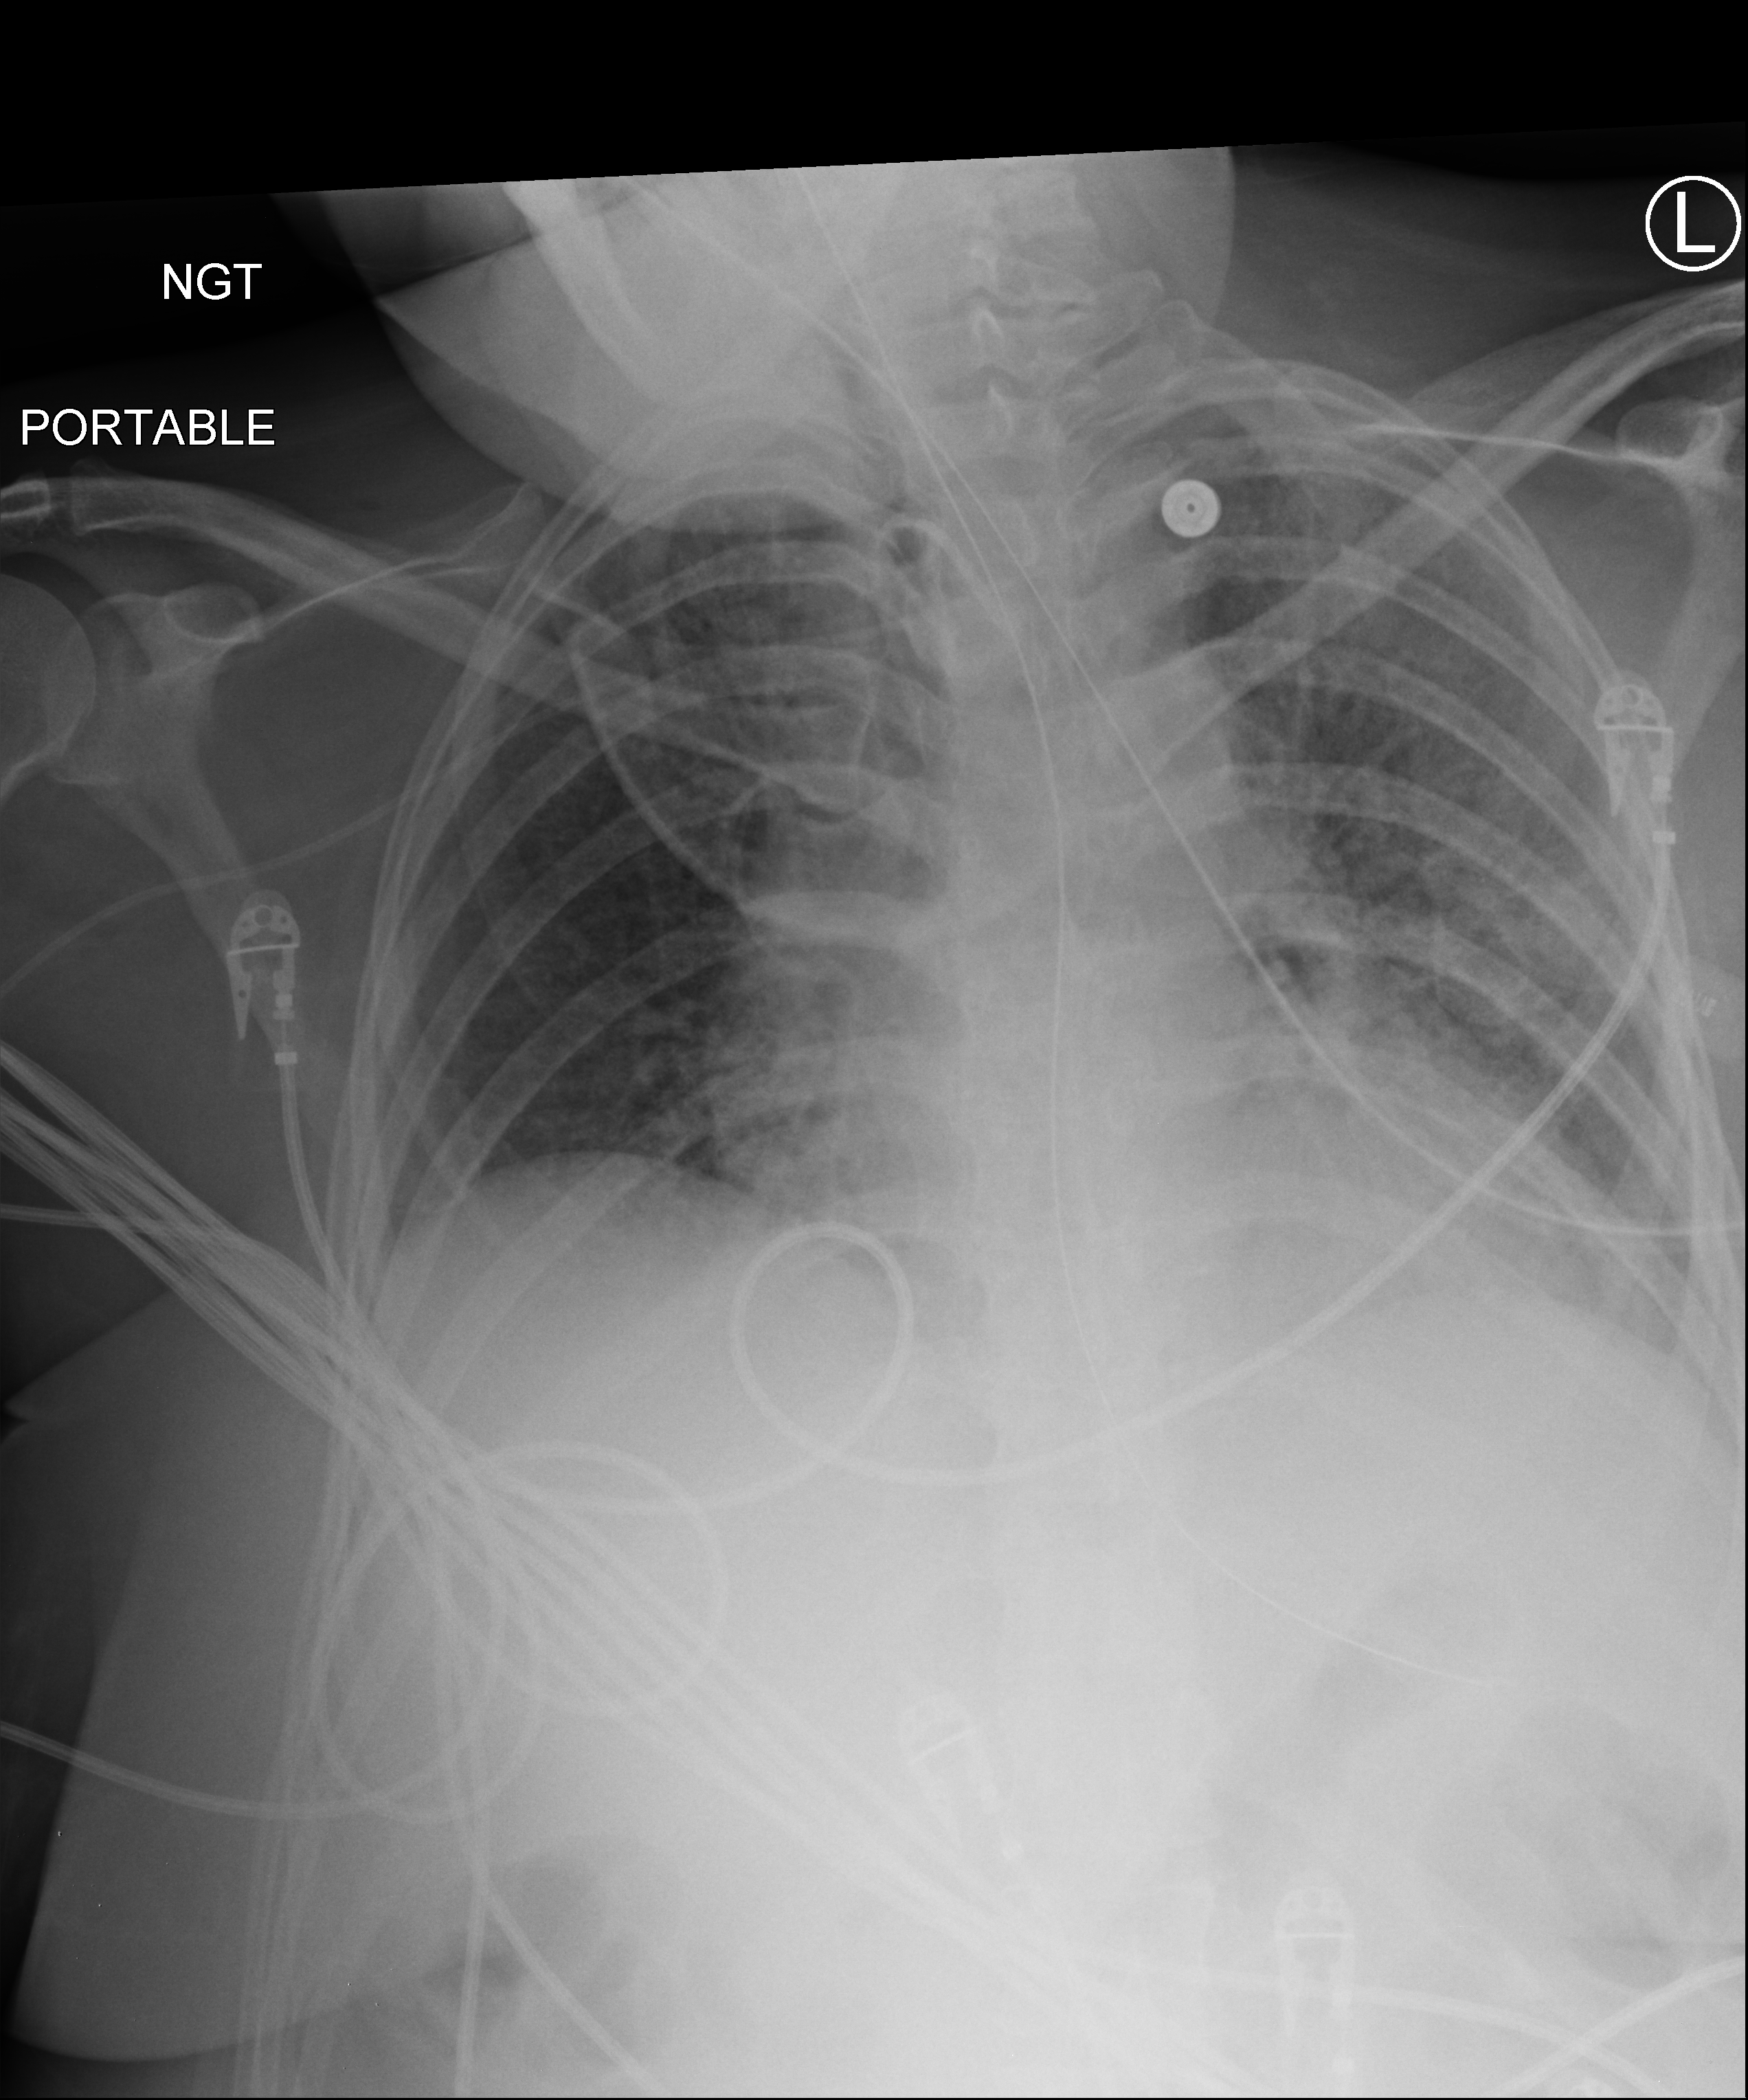
Portable chest radiograph, anteroposterior (AP) projection. Female patient hospitalised with COVID-19, age 18–59 years.
Admission-level facts for this patient (not findings on this image; timing relative to this image not recorded): chronic kidney disease (admission record): no; mechanically ventilated during this hospital stay: yes.